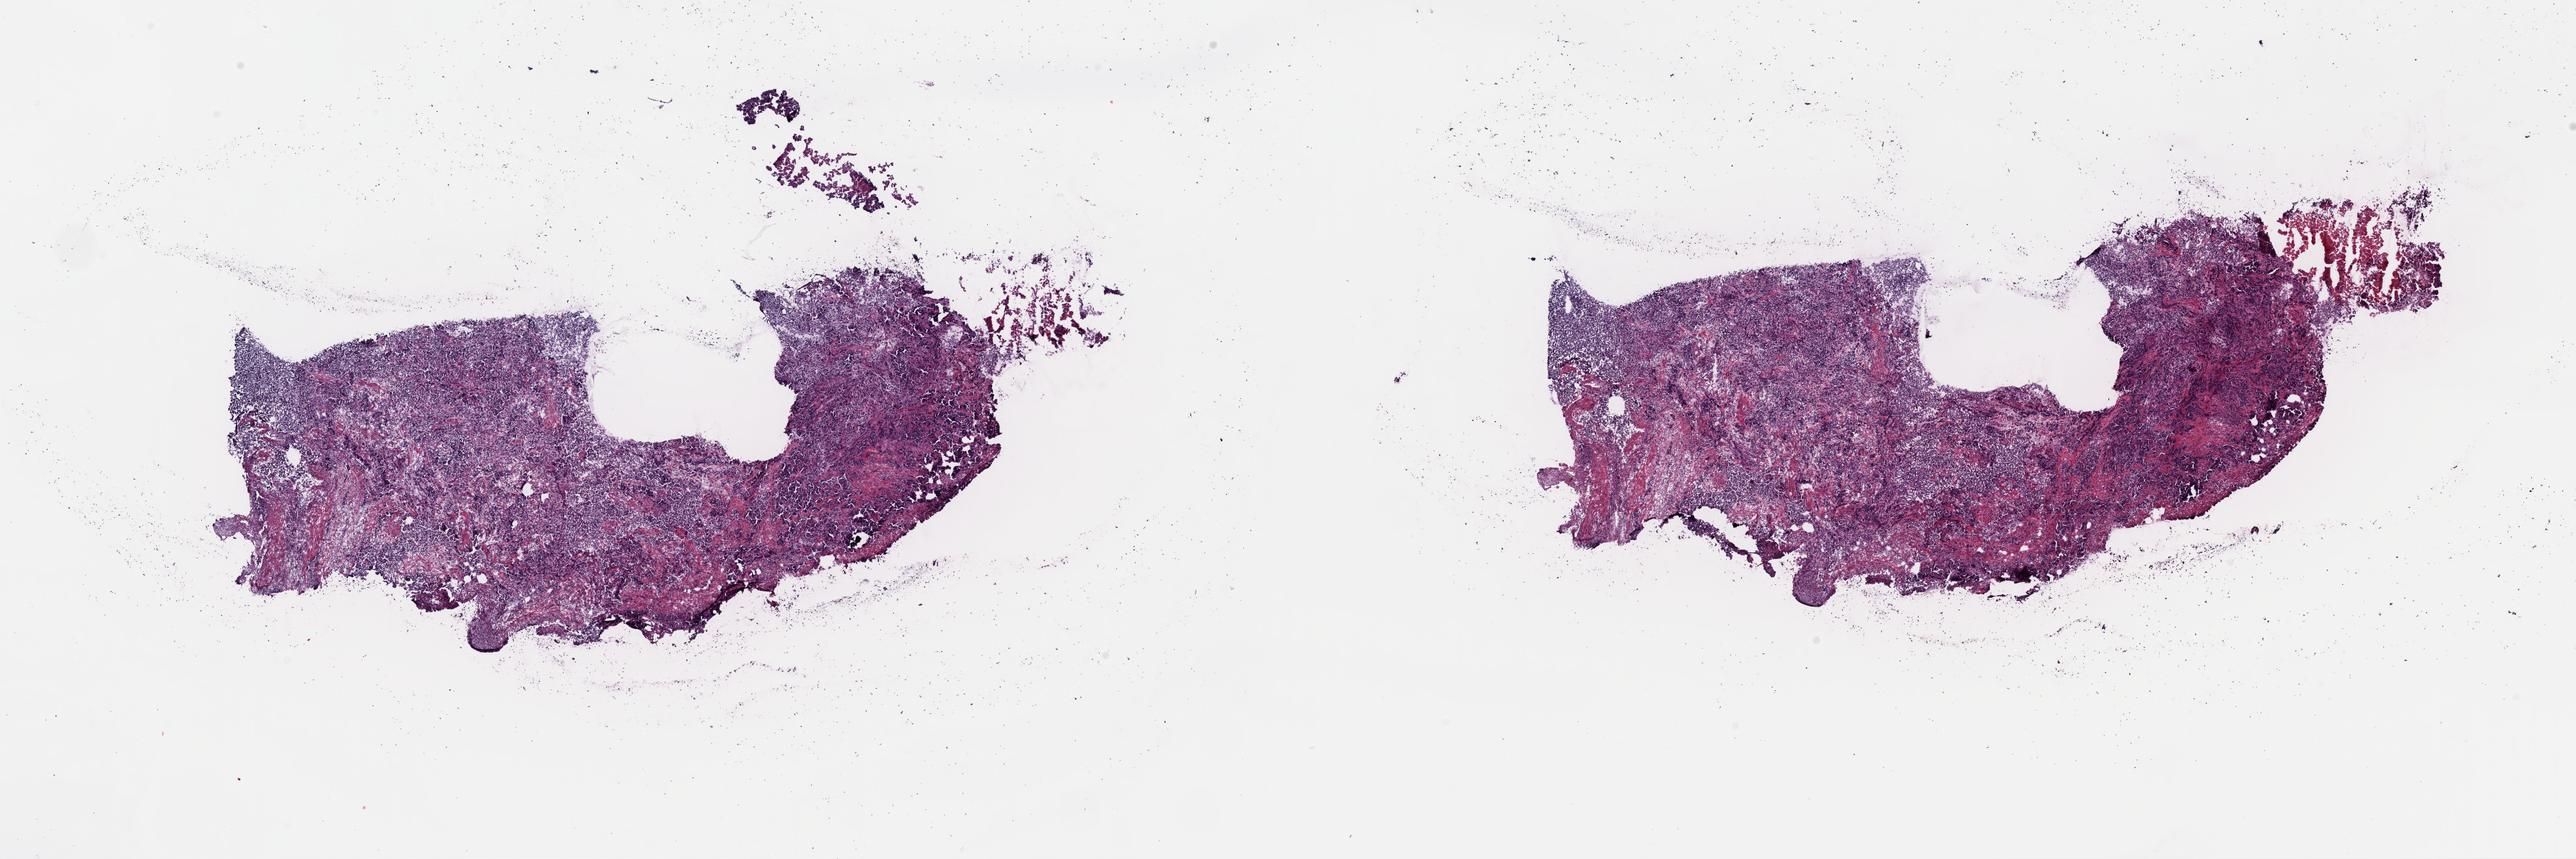
Whole-slide histology image, H&E-stained — shown as a low-resolution overview of the whole scanned area (about 28.2 x 9.4 mm, slide scanned at 40x), frozen section, sample: primary tumour, uterus. Female patient; age at initial diagnosis 63 years. Histologic grade: G3 (poorly differentiated). Pathologist review of this section (percent, as recorded): tumour cells 60%, tumour nuclei 80%, normal cells 20%, stromal cells 20%, necrosis 10%. Inflammatory infiltration, as recorded: lymphocyte infiltration 6%, monocyte infiltration 0%, neutrophil infiltration 0%.
* diagnosis: Endometrioid adenocarcinoma, NOS (endometrium)
* FIGO stage: IC